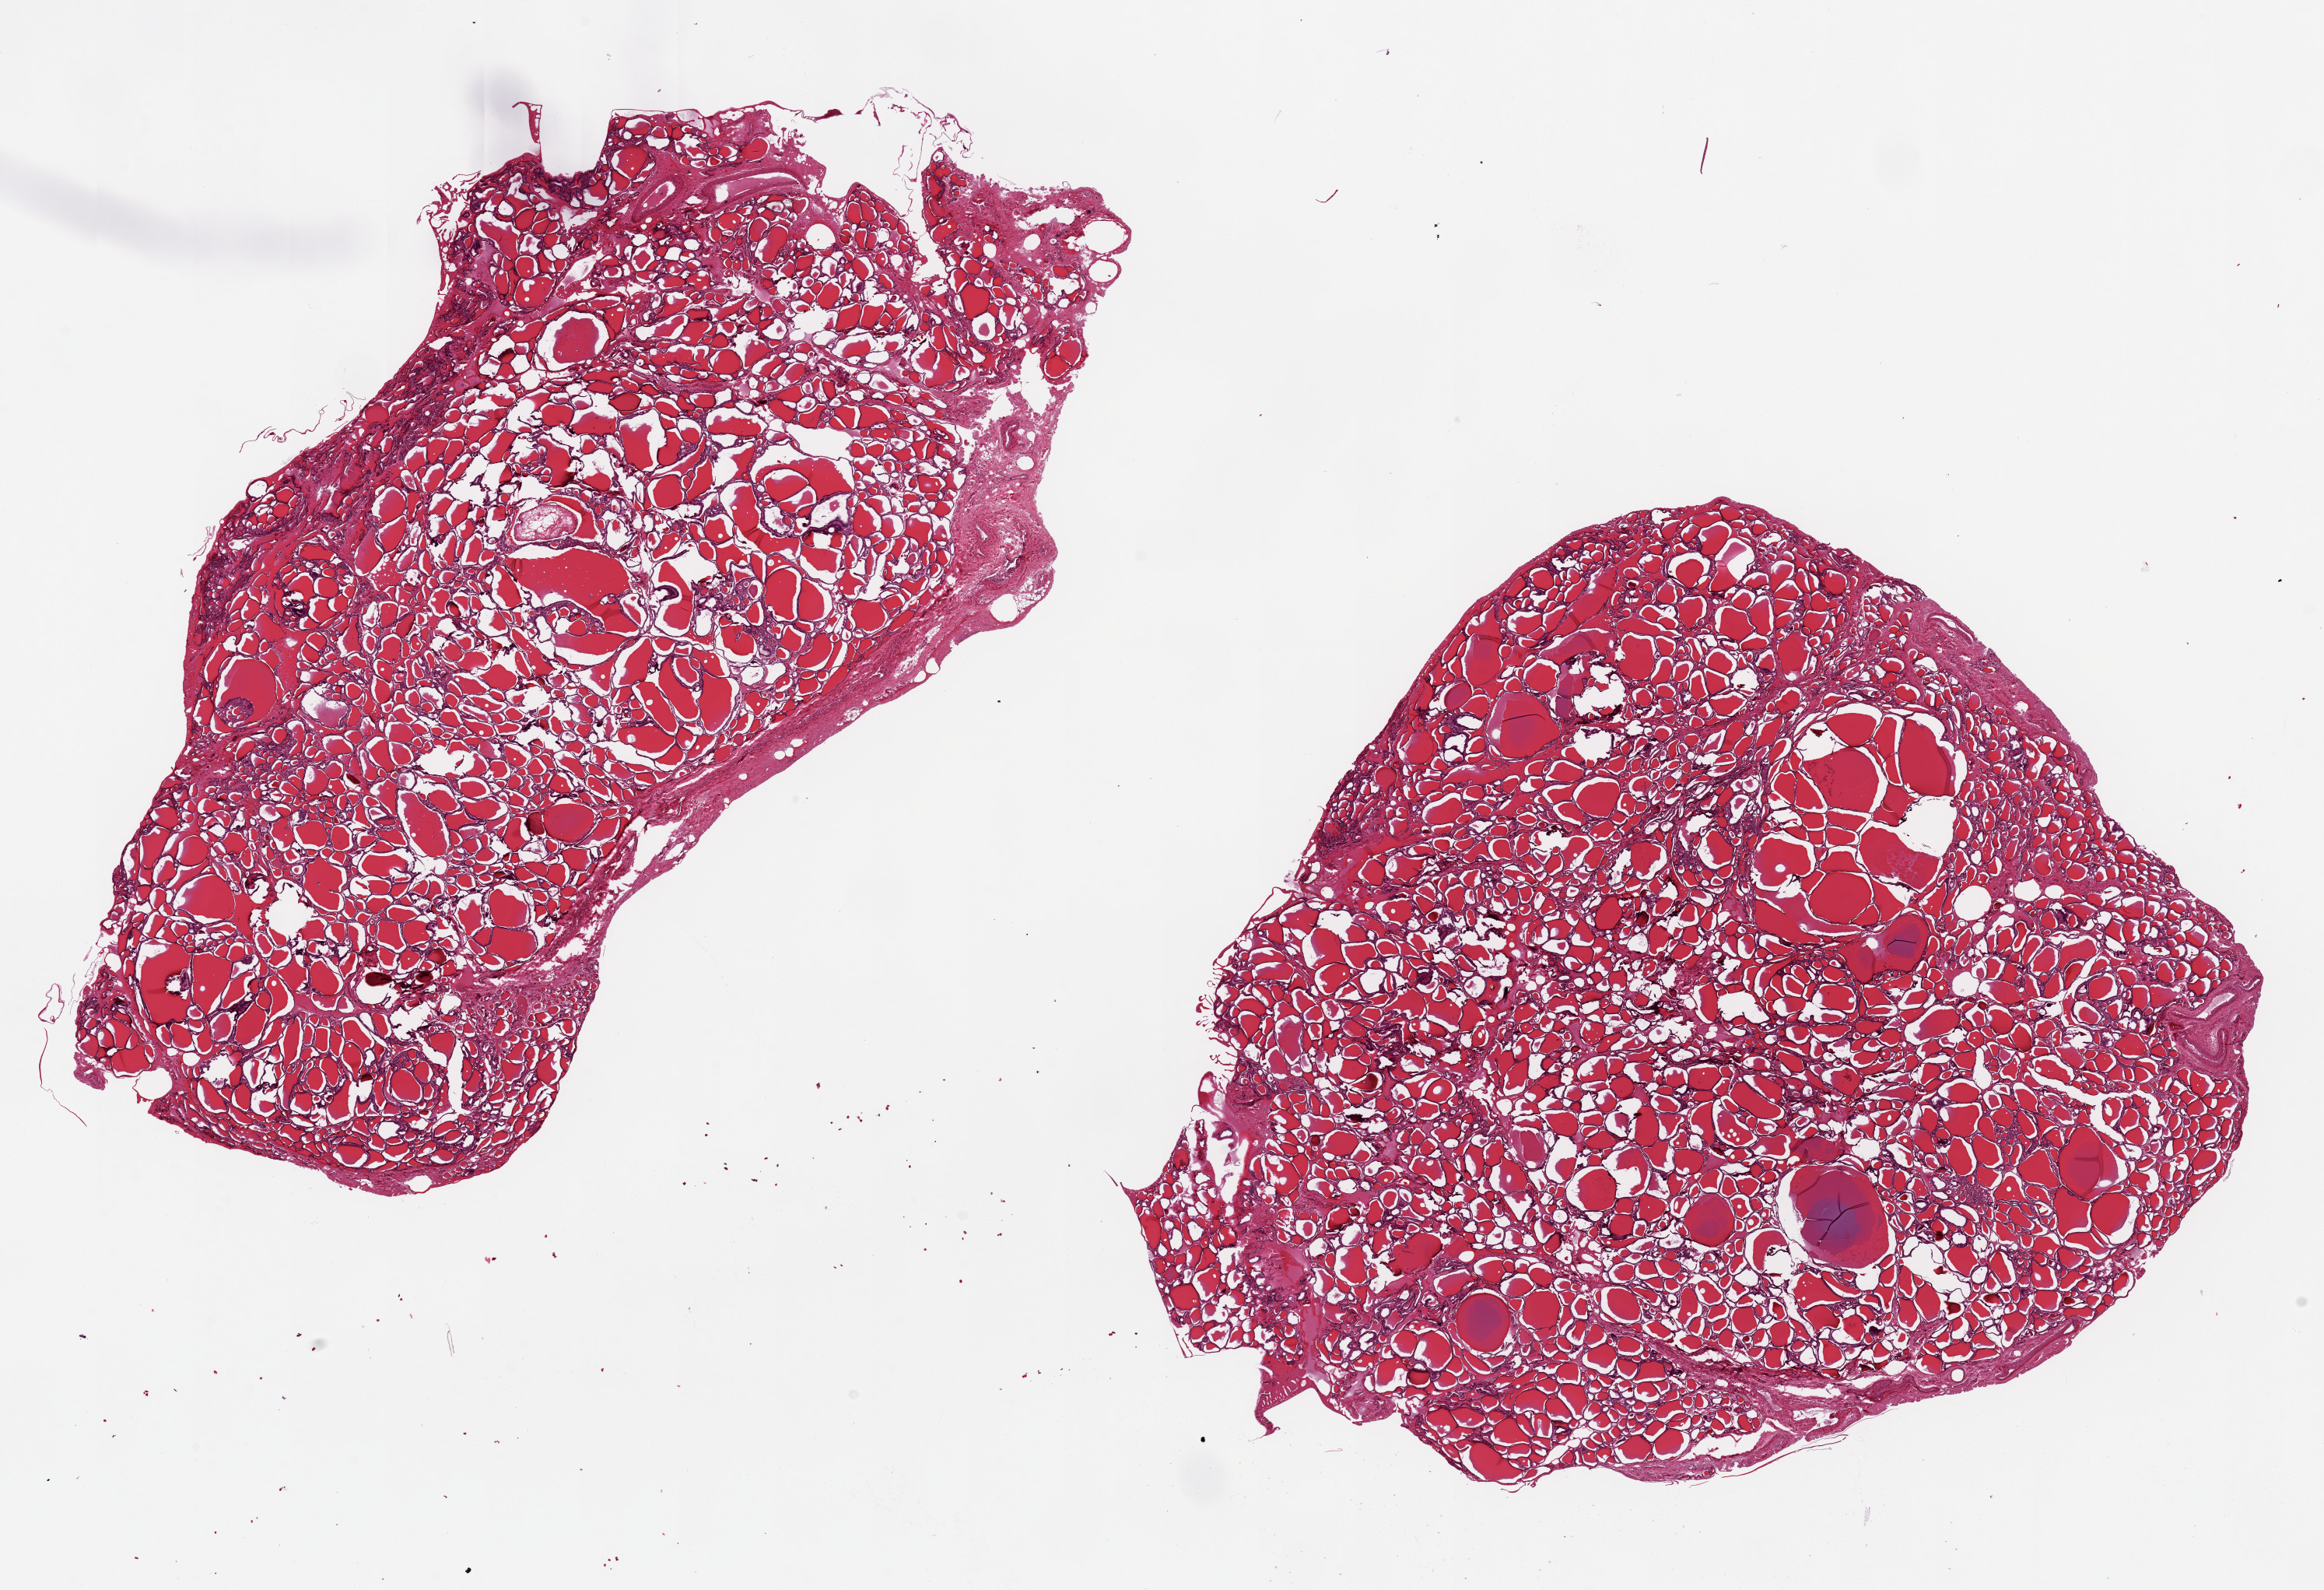
Haematoxylin and eosin whole-slide image, shown as a low-resolution overview of the whole scanned area (about 23.6 x 16.2 mm, slide scanned at 20x); PAXgene-fixed paraffin-embedded (PFPE) section; target tissue: thyroid; donor tissue sample. Donor sex: female.
Review note (as recorded): 2 pieces ~10x7mm, ~2.5mm adenomatoid nodule.colloid cyst.